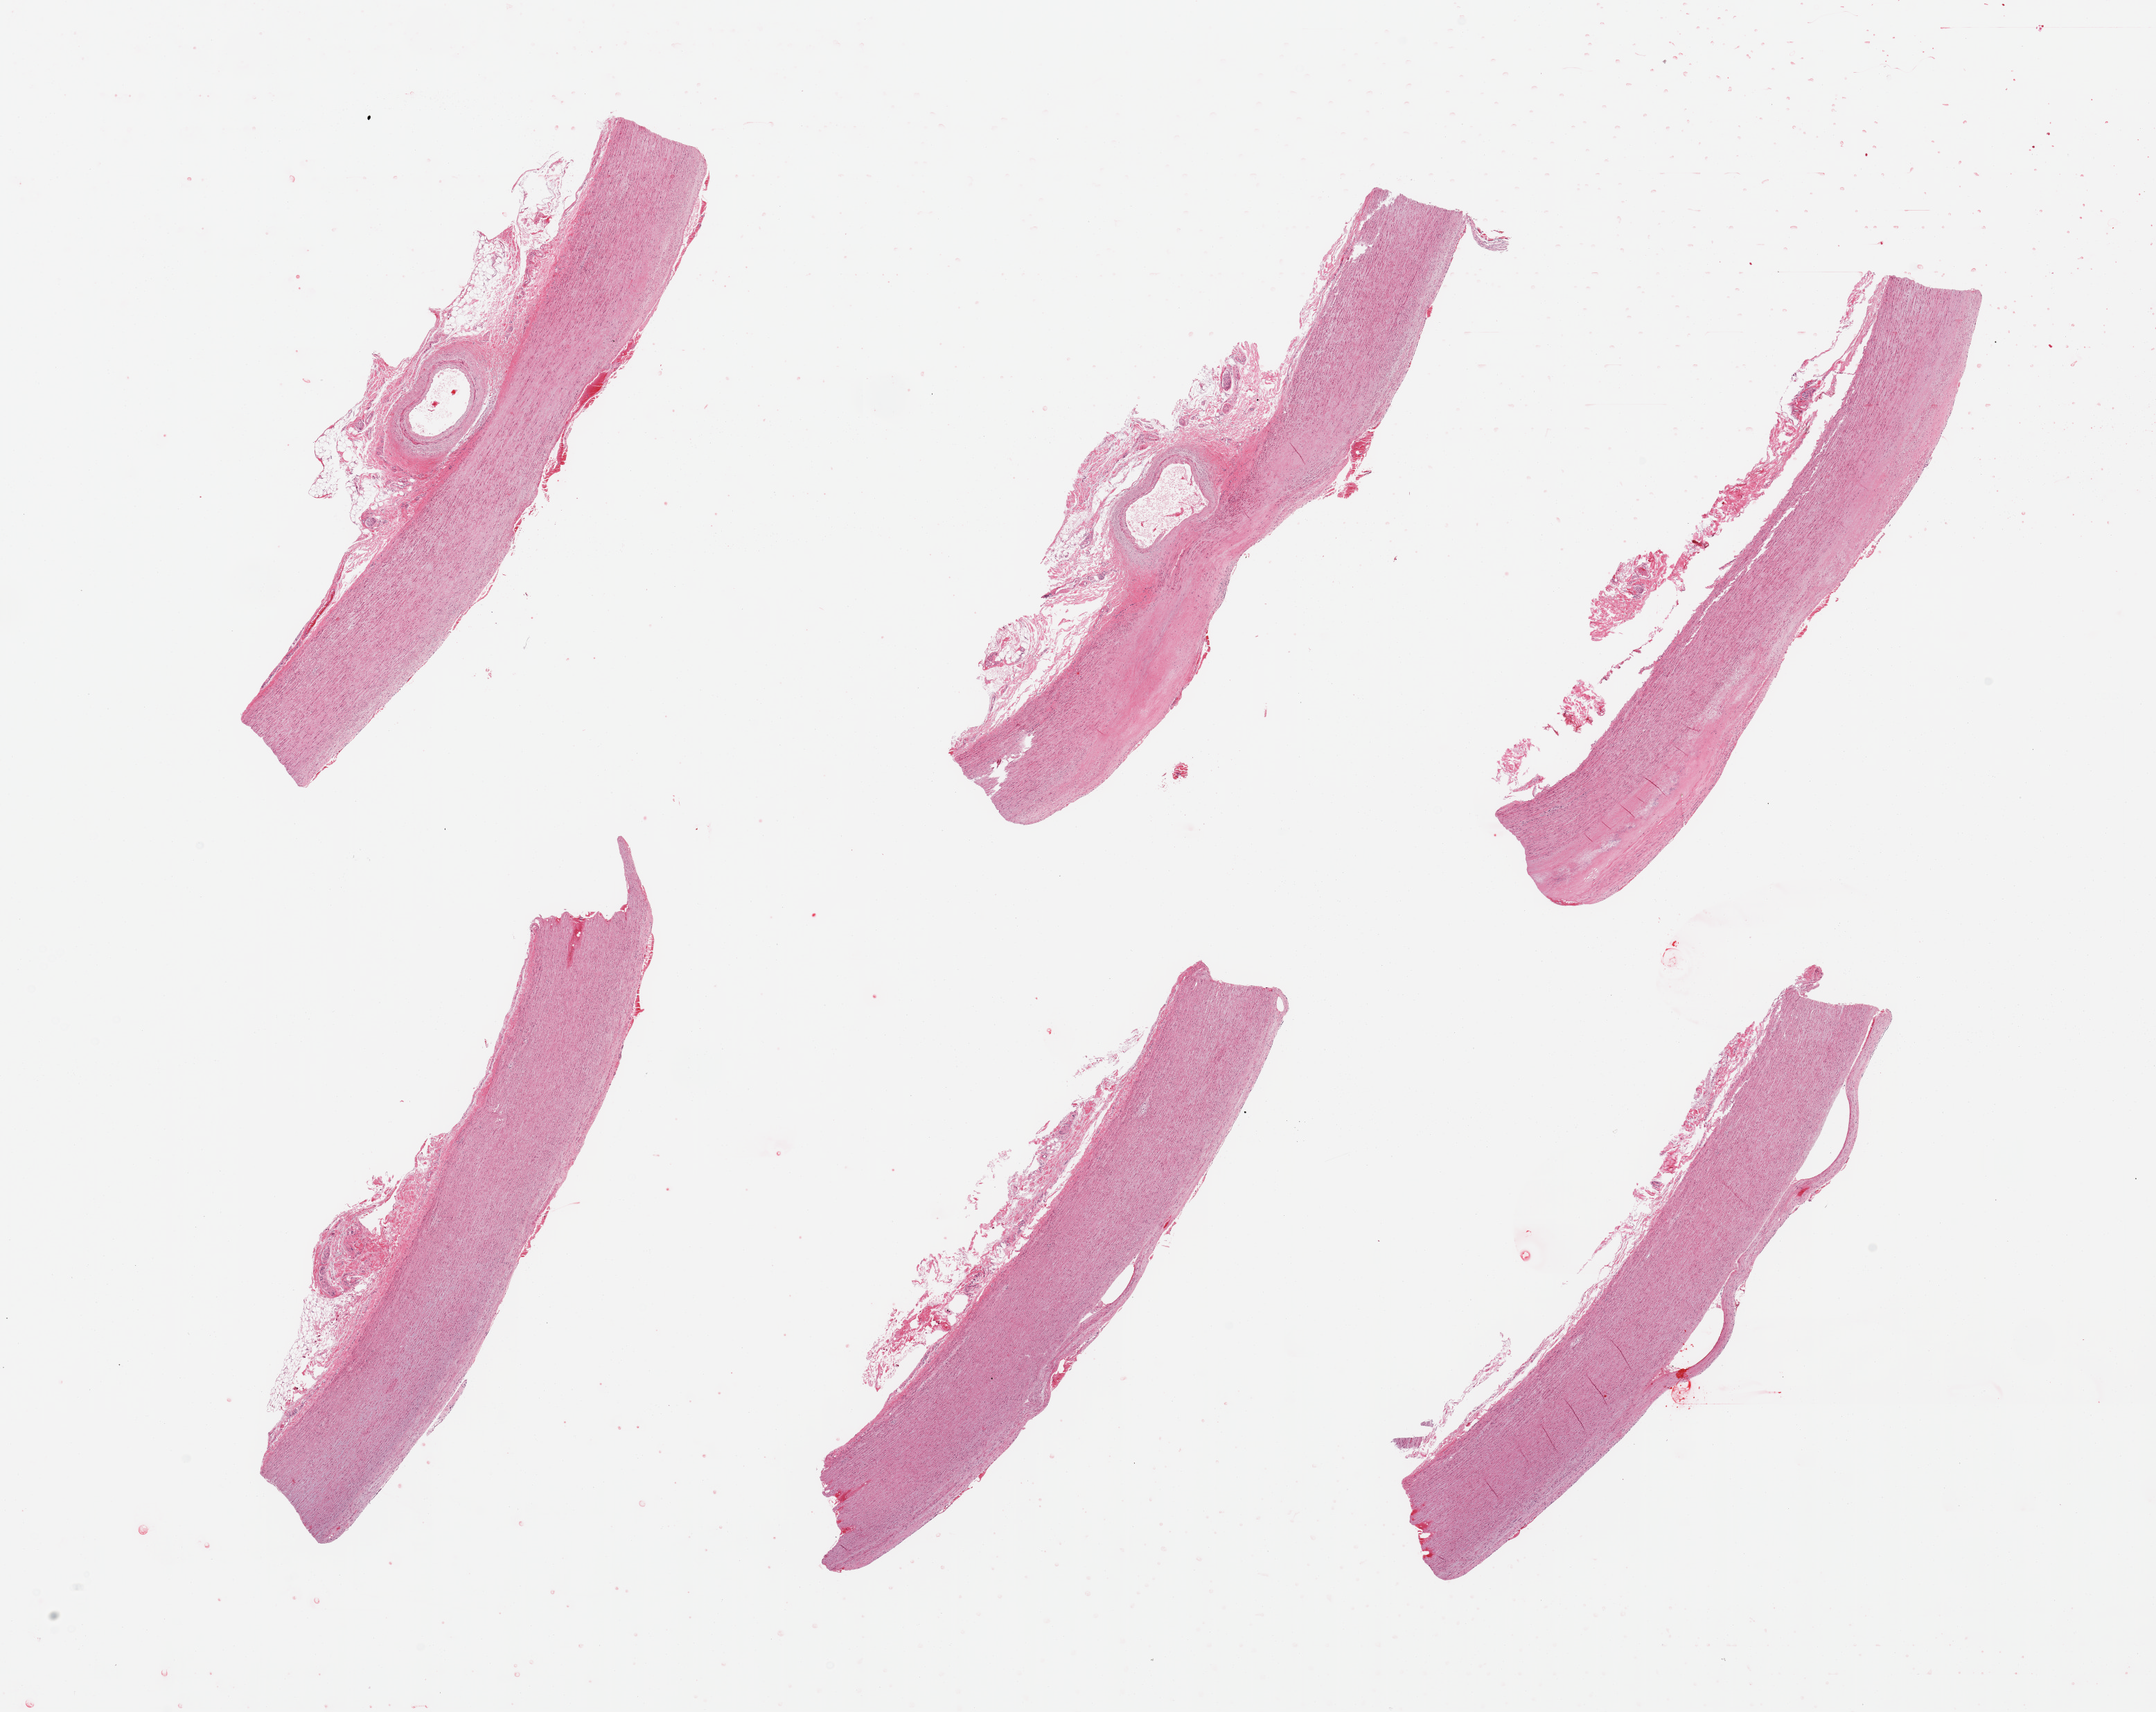
Haematoxylin and eosin whole-slide image — shown as a low-resolution overview of the whole scanned area (about 24.6 x 19.5 mm); PAXgene-fixed paraffin-embedded (PFPE) section; target tissue: aorta; tissue donor sample. Donor: female.
Review note (as recorded): 6 pieces; atherosclerosis.